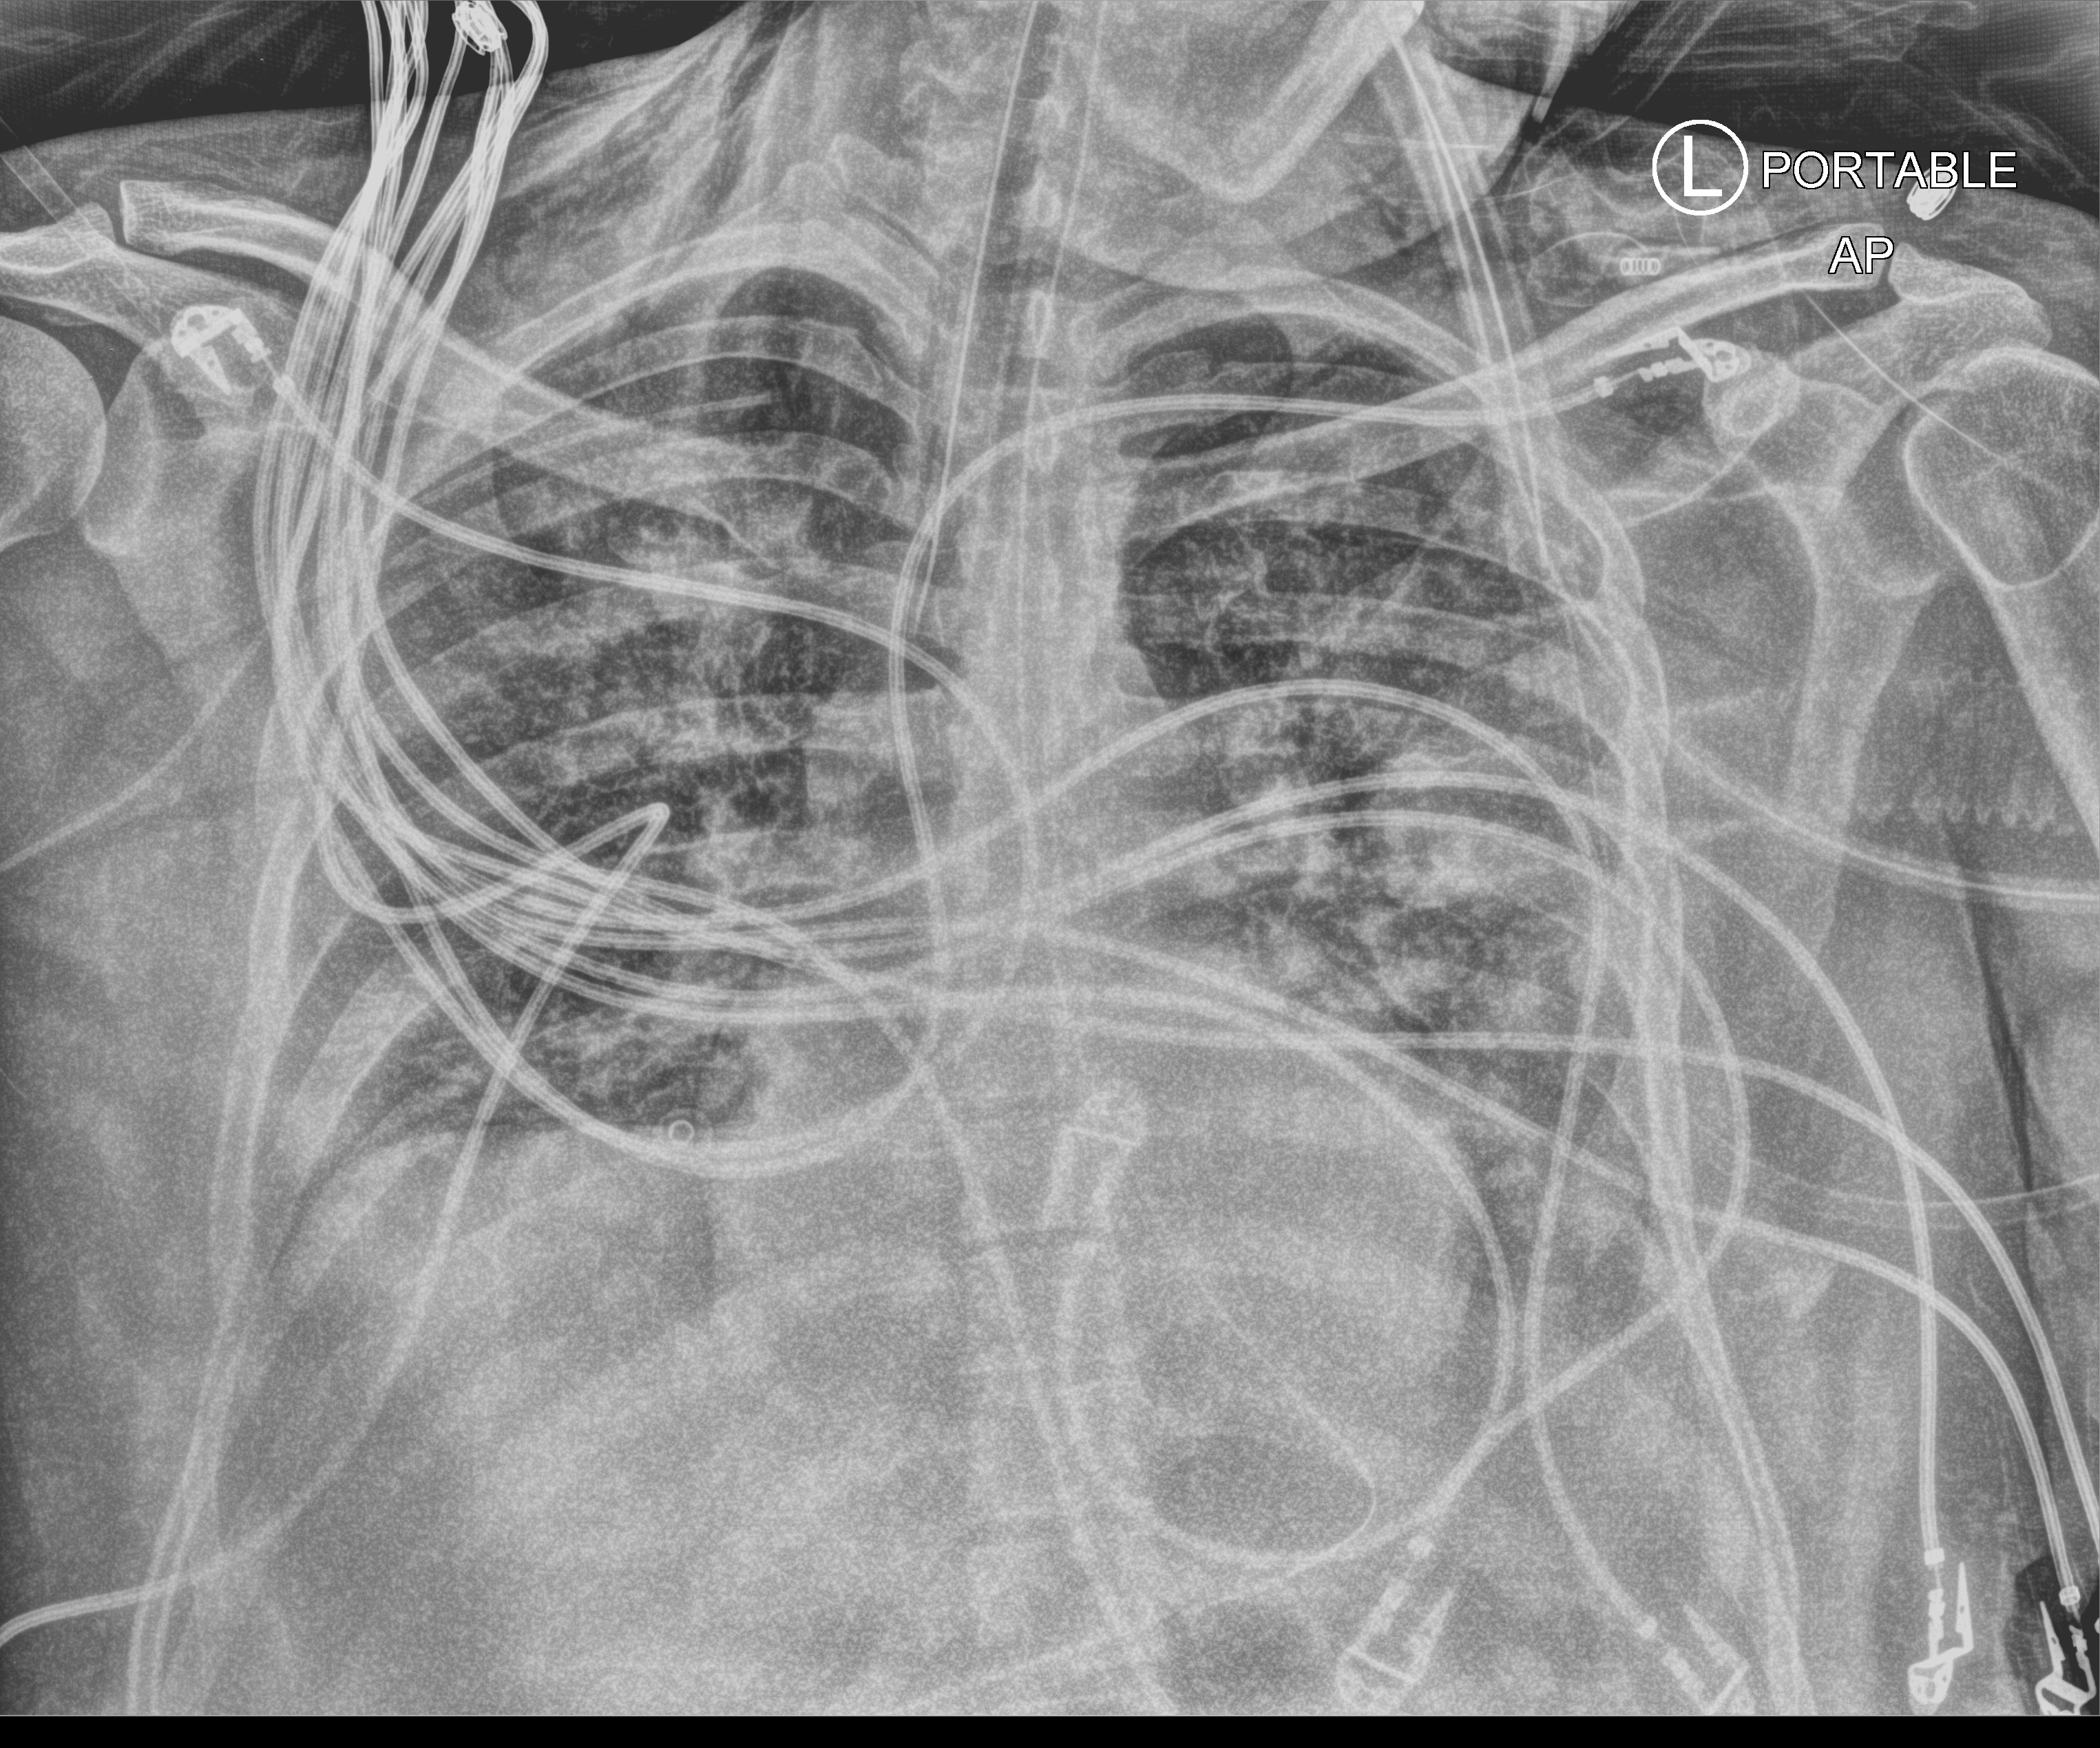
Portable chest radiograph, anteroposterior (AP) projection. Male patient hospitalised with COVID-19, age 18–59 years.
Hospital-stay facts (about this admission, not read from this image; timing relative to this image not recorded): smoking status (admission record): never.